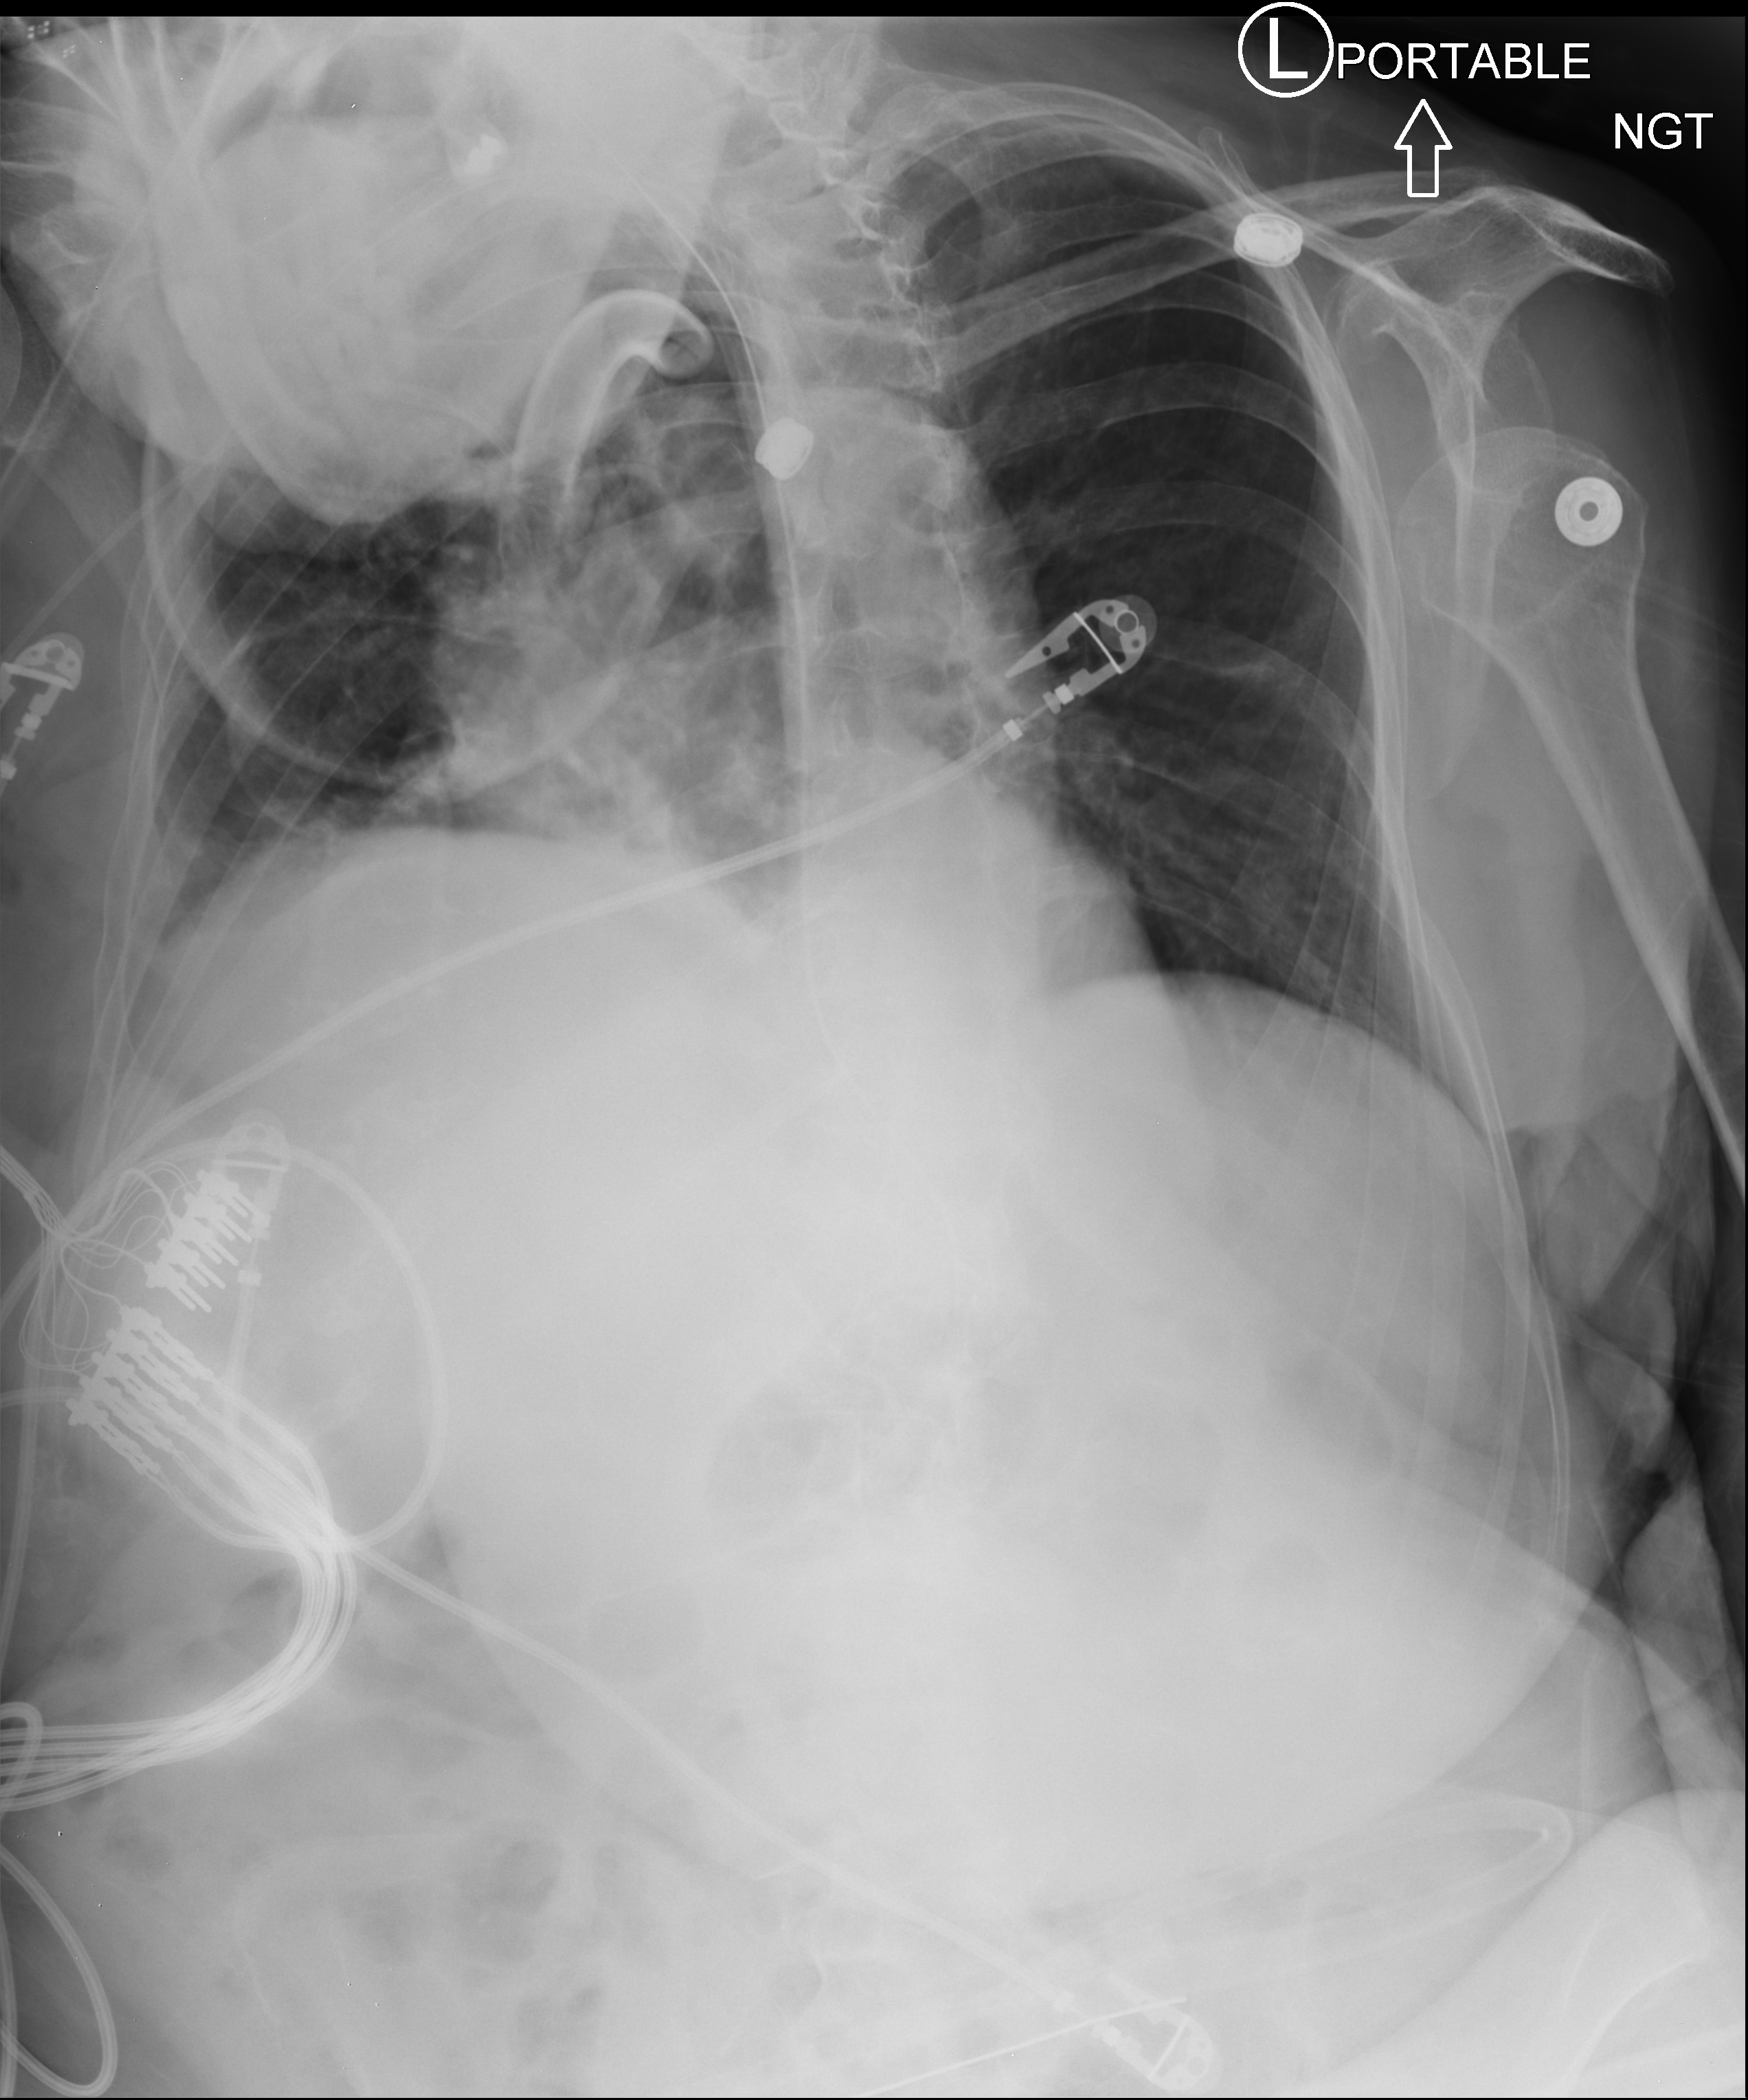
Bedside abdomen radiograph (computed radiography), anteroposterior (AP) projection. Patient hospitalised with COVID-19; female, aged 75–90 years.
Hospital-stay facts (about this admission, not read from this image; timing relative to this image not recorded):
- mechanically ventilated during this hospital stay: yes